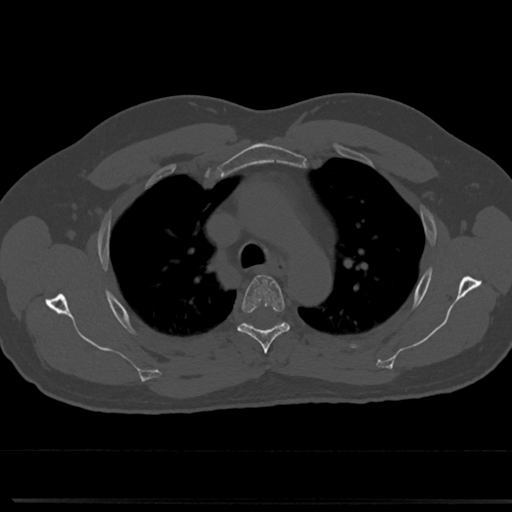
CT including the spine, one axial slice; slice 541 of 817 in the series (ordered by position); bone window (W 1800 / L 400 HU); 0.5 mm slice thickness; 512 × 512 image matrix. Male patient, age 61 years. From the clinical record (not read from this slice): primary cancer: prostate.
Outlined on this slice (semi-automatic segmentation, software-assisted and operator-edited):
- T4 vertebra: bounding box [x1, y1, x2, y2] px = [237, 275, 291, 352]
- T5 vertebra: [247, 322, 282, 325]